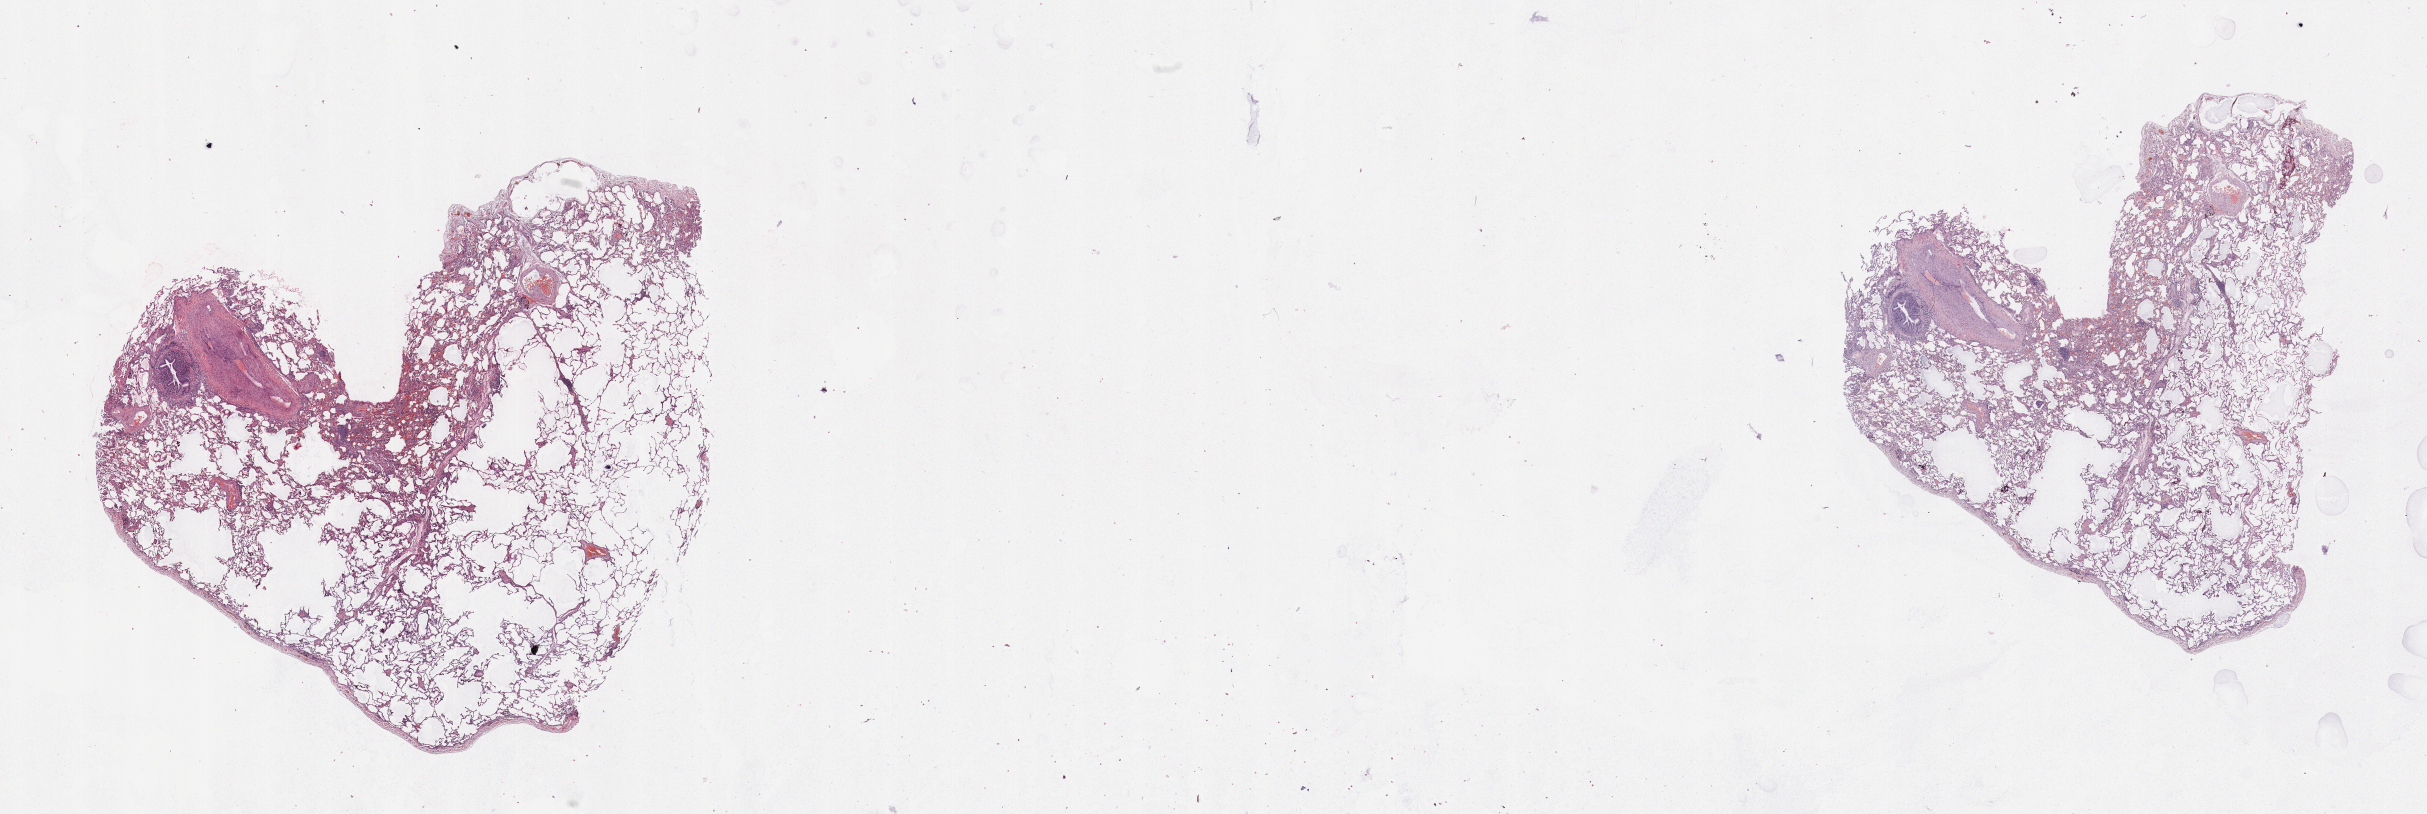
Digitized H&E tissue section (whole slide), whole scanned area (about 38.4 x 12.9 mm, slide scanned at 20x) shown as a low-resolution overview. Normal (non-tumour) tissue sample, lung. Male, 67 y/o.
* this section: normal (non-tumour) tissue from the same patient
* patient diagnosis: Adenocarcinoma, NOS